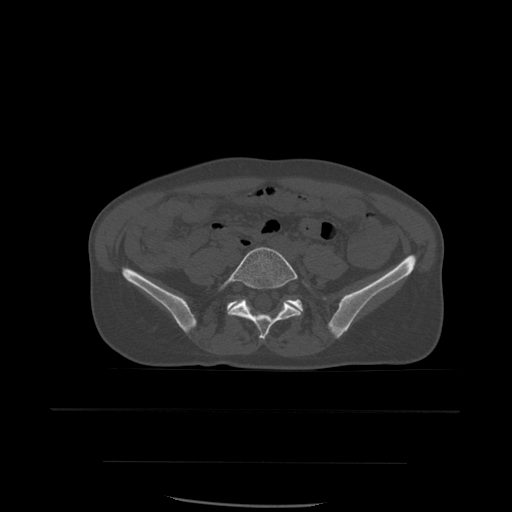
CT including the spine, one axial slice; slice 144 of 574 in the series (ordered by position); bone window (W 1800 / L 400 HU); 1.25 mm slice thickness; 512 × 512 image matrix, field of view 392 × 392 mm. Patient age 48 years. From the clinical record (not read from this slice): primary cancer: lung; vertebrae with lytic lesions (as recorded): T11.
Outlined on this slice (semi-automatic segmentation, software-assisted and operator-edited):
- L5 vertebra: bounding box <219,247,310,340> (left, top, right, bottom; pixels)